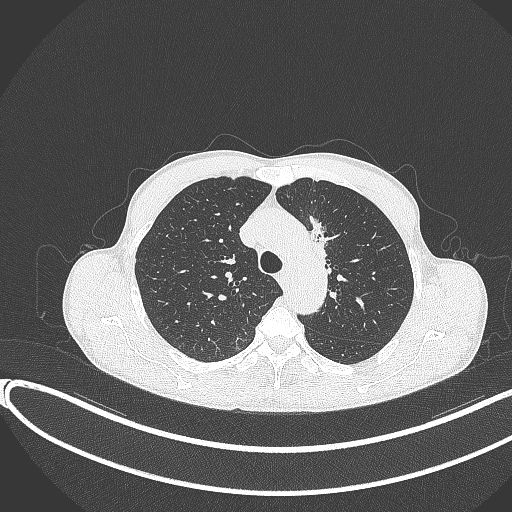
Chest CT, one axial slice. Slice 278 of 374 in the series (ordered by position). 120 kVp. Lung window (W 1500 / L -600 HU). 1 mm slice thickness. 512 × 512 image matrix, field of view 400 × 400 mm. Patient: male, 58 years. Case-level facts recorded for this patient, not image findings: clinical TNM (as recorded): T1c N1 M0.
Structures marked on this image (bounding box drawn by a radiologist):
- lung tumour (recorded histology: adenocarcinoma): bounding box (x1, y1, x2, y2) in pixels: (301, 214, 334, 271)